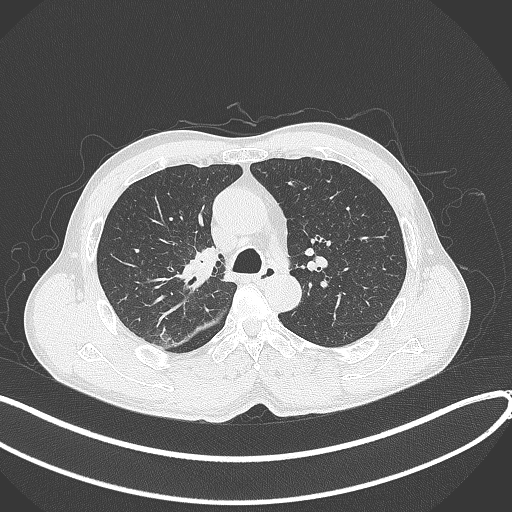
Chest CT, one axial slice; position 263 of 409 along the scan axis; reconstruction kernel B70f; lung window (W 1500 / L -600 HU); 512 × 512 image matrix. Male patient, age 53 years. From the clinical record (not read from this slice): clinical TNM (as recorded): T1b N0 M0.
Annotated regions visible in this slice (rectangle marked by the reading radiologist):
- lung tumour (recorded histology: squamous cell carcinoma): box from (x=180, y=239) to (x=225, y=292) px